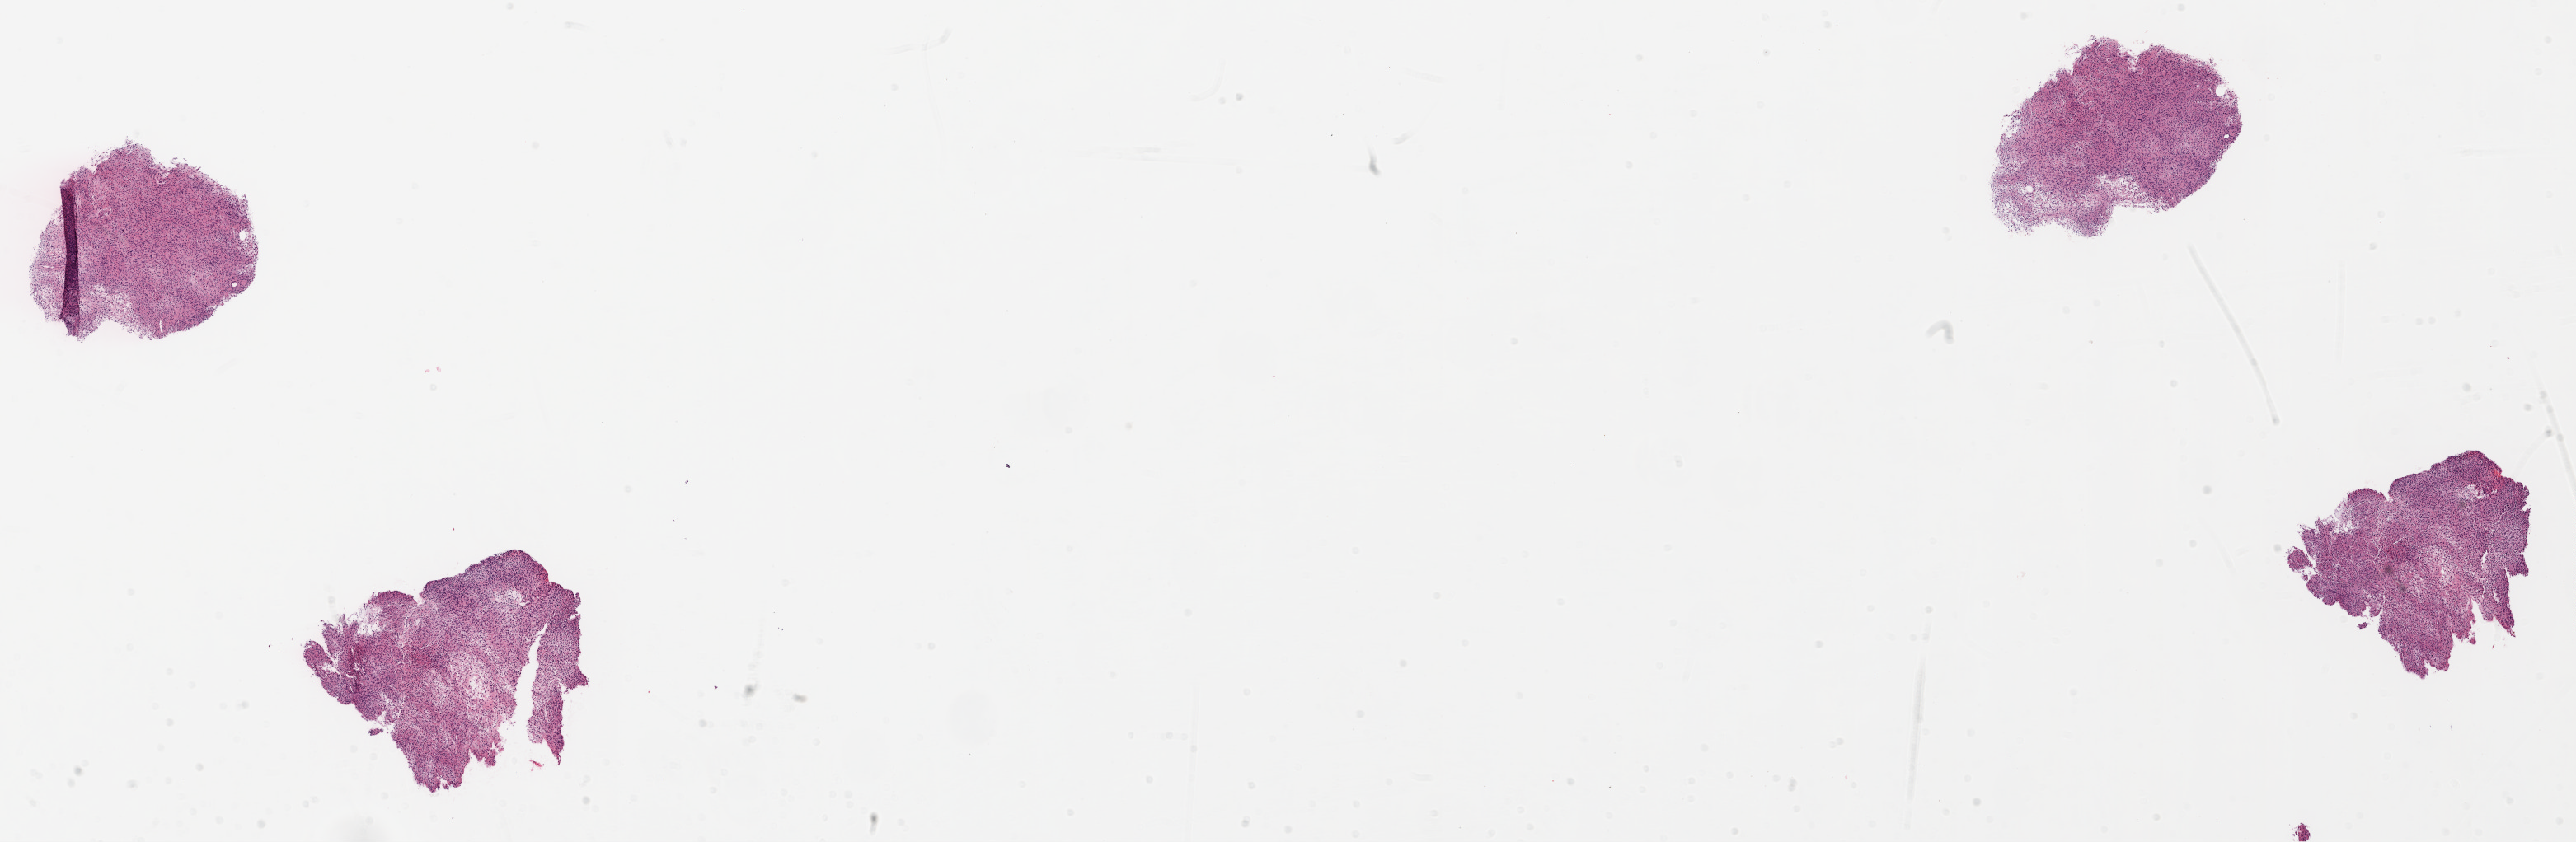
Hematoxylin and eosin (H&E) stained whole-slide image — low-resolution overview of the scanned area, about 25.1 x 8.2 mm (acquisition: 20x scan), formalin-fixed paraffin-embedded (FFPE) diagnostic section, primary tumour sample from the brain. Patient: female, age at initial diagnosis 58 years.
Histologic diagnosis: Glioblastoma.